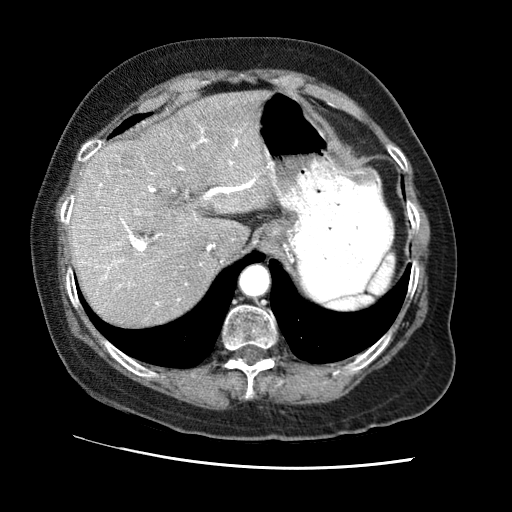
Contrast-enhanced abdominal CT (liver protocol), one axial slice; 120 kVp; soft-tissue window (W 400 / L 40 HU); 2.5 mm slice thickness; 512 × 512 image matrix, field of view 340 × 340 mm. From the clinical record (not read from this slice): diagnosis: hepatocellular carcinoma (patient treated with transarterial chemoembolisation; whether this scan precedes or follows treatment is not stated here); TNM stage (as recorded): Stage-II; Child-Pugh class: A; tumour differentiation: no biopsy; tumour nodularity: multinodular.
Outlined on this slice (semi-automatic segmentation, software-assisted and operator-edited):
- liver parenchyma outside the tumour (the mass and vessels are separate outlines, so this box may not span the whole liver): bounding box [x1, y1, x2, y2] px = [70, 90, 272, 326]
- mass: [97, 142, 144, 183]
- liver vessels: [81, 128, 257, 305]